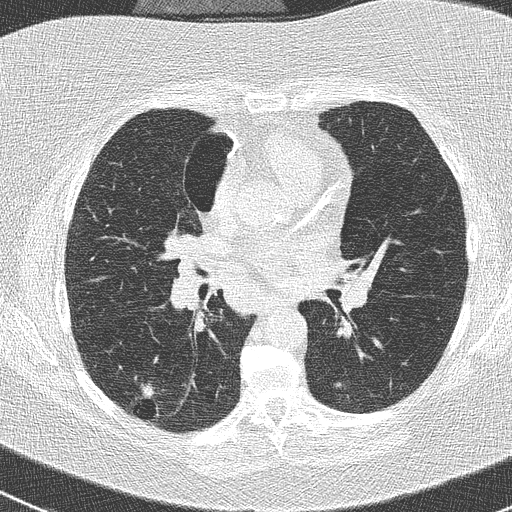
Low-dose screening chest CT, axial slice; baseline annual screen; lung window (W 1500 / L -600 HU); 2 mm slice thickness; lung (sharp) reconstruction kernel (B50f); slice 124 of 261 in the series. Female, age 74 years at enrolment.
- Expert reader's lesion annotation, box from (x=121, y=373) to (x=175, y=431) px.
- The screening reader recorded 3 non-calcified nodules or masses ≥4 mm on this exam (right lower lobe, right upper lobe, left lower lobe); which of them this box marks is not recorded.